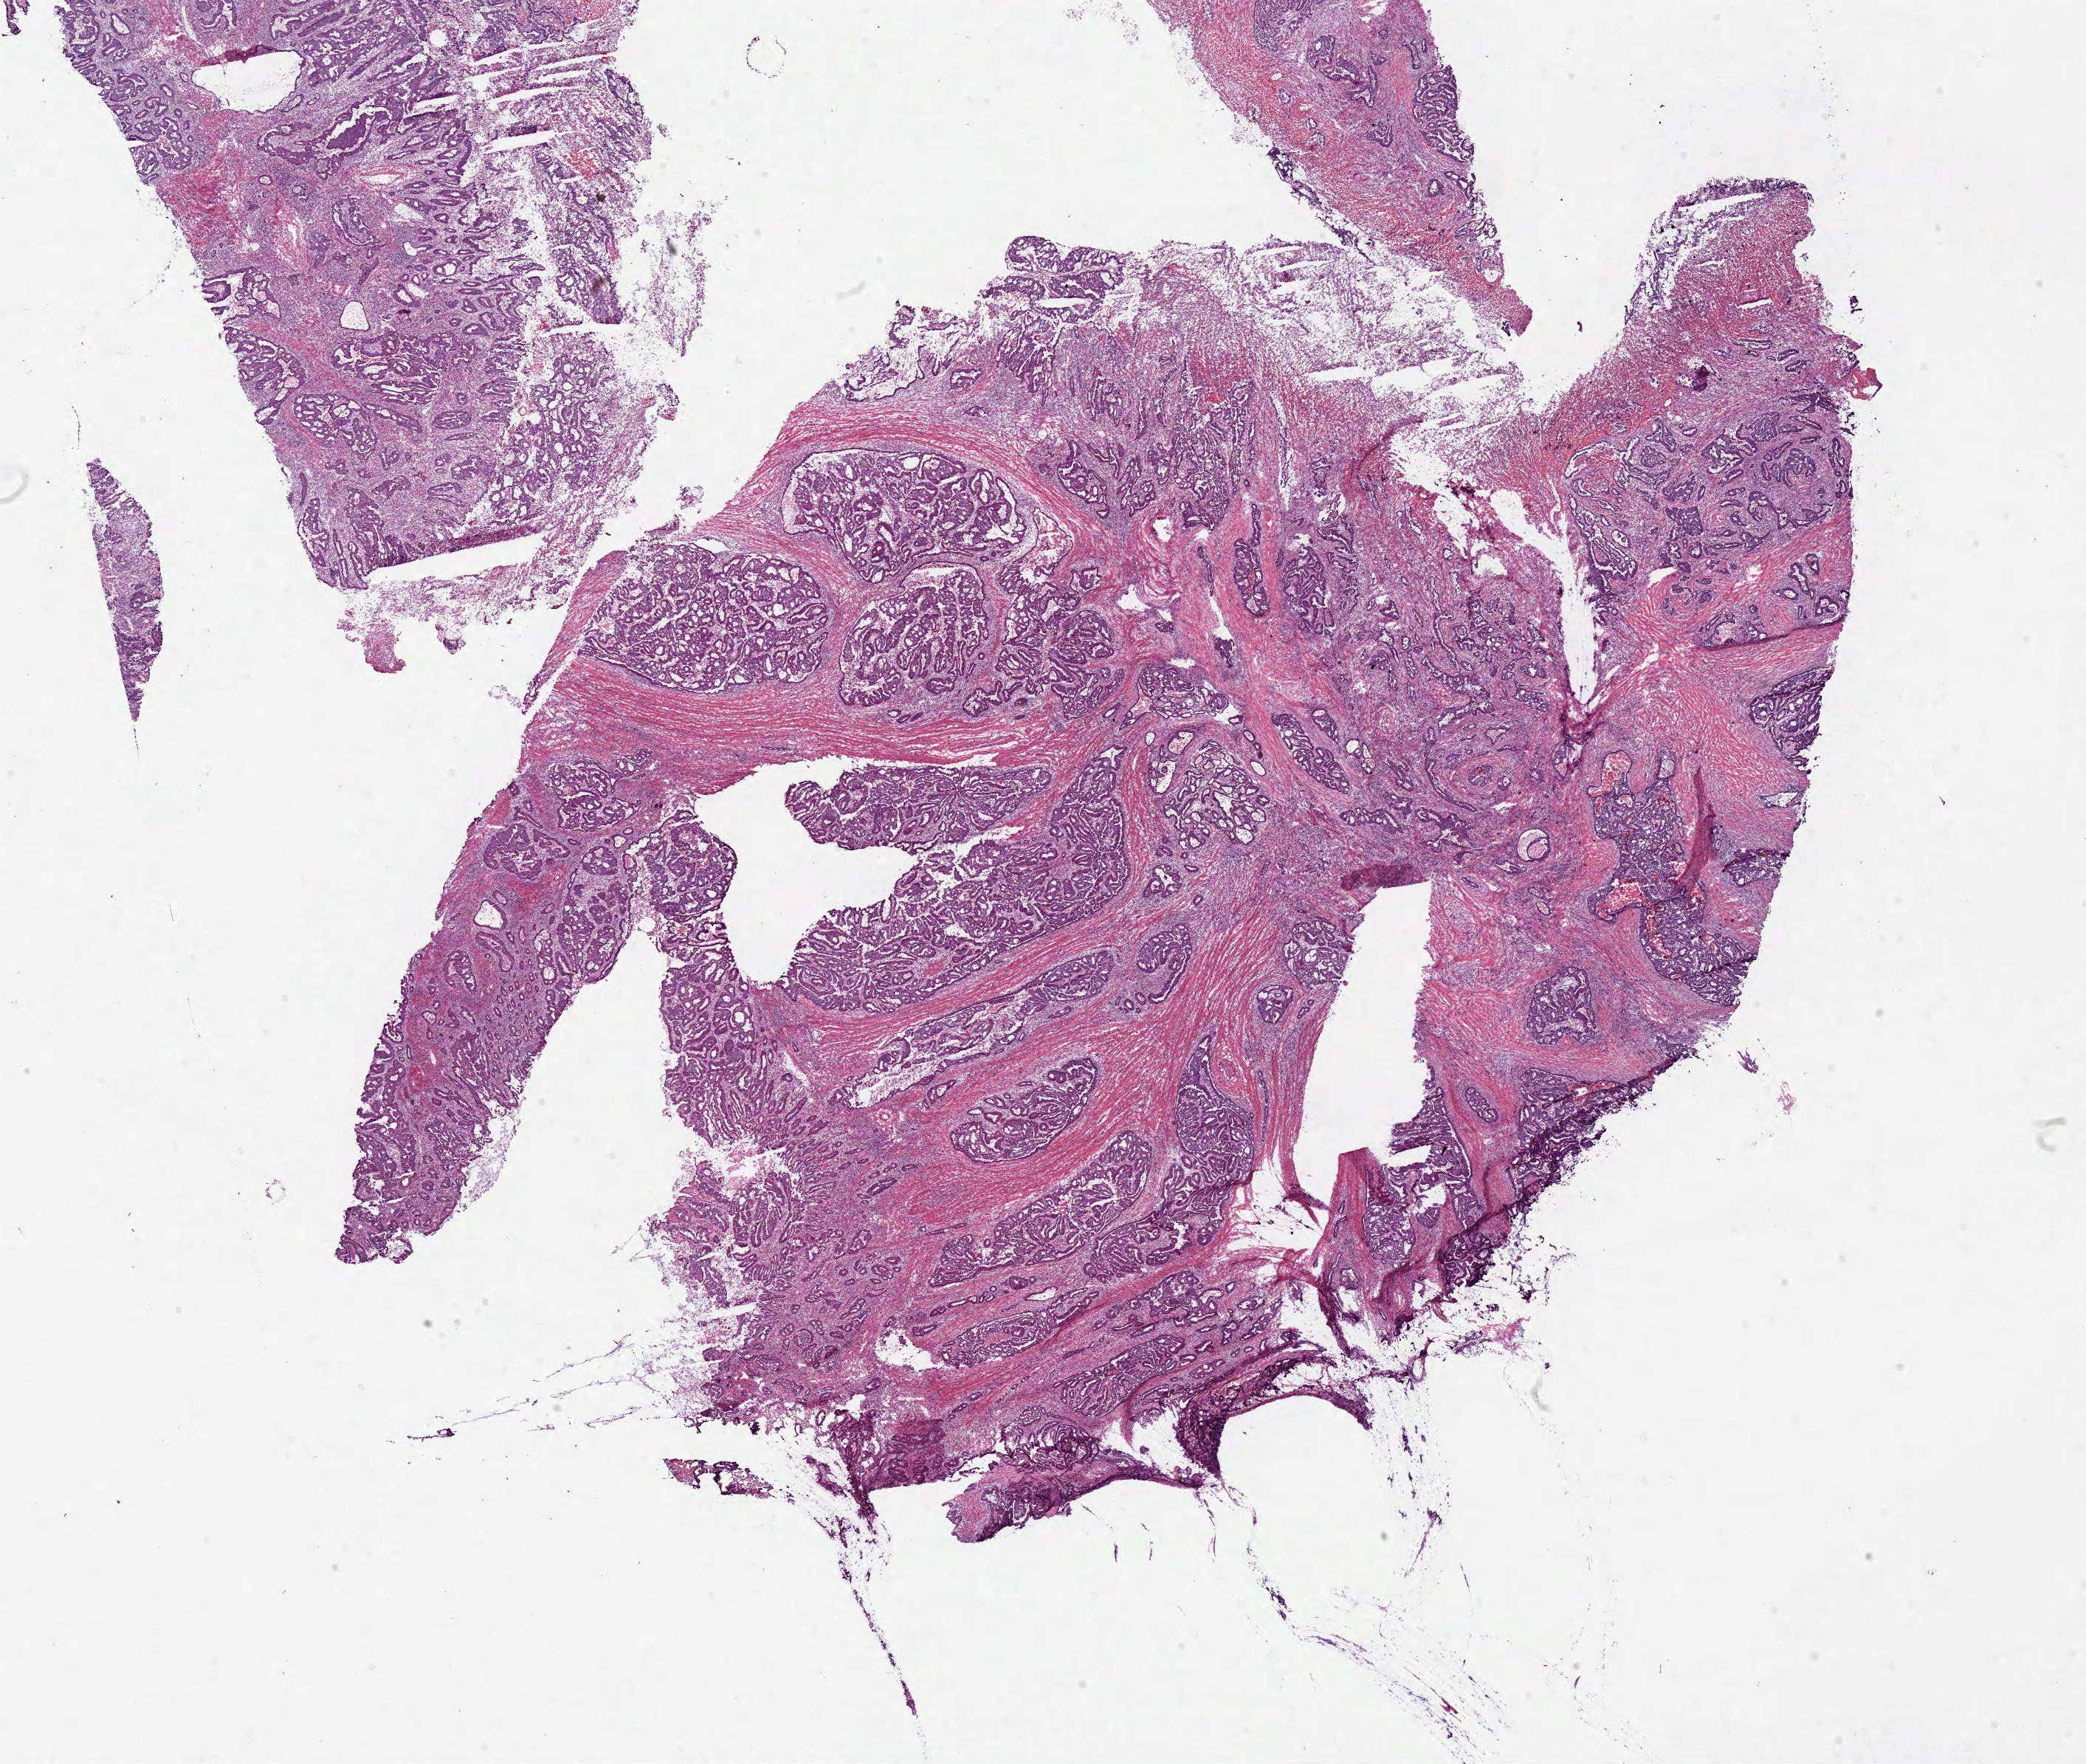
Hematoxylin and eosin (H&E) stained whole-slide image — a low-resolution overview of the entire scanned area, about 22.3 x 18.8 mm; frozen section; sample: primary tumour, colon. Female patient; age at initial diagnosis 46 years. Pathologist review of this section (percent, as recorded): tumour cells 83%, tumour nuclei 80%, normal cells 0%, stromal cells 15%, necrosis 2%.
* lymph nodes positive (case pathology): 0 of 14 examined
* histologic diagnosis: Adenocarcinoma, NOS (sigmoid colon)
* TNM: T3 N0 M0
* AJCC pathologic stage: IIA (6th edition)